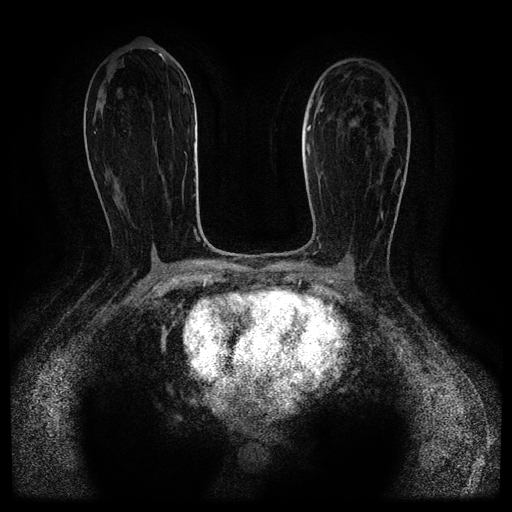
Breast MRI (dynamic contrast-enhanced, multi-phase), one axial slice; position 54 of 116 along the scan axis; dynamic contrast-enhanced series, time point 2 of 5 at this slice position (early post-contrast); 1.5 T; TE 2.6 ms, TR 5.3 ms; 2 mm slice thickness; 512 × 512 image matrix. Female patient, age 52 years.
Annotated regions visible in this slice (semi-automatically segmented with operator editing):
- breast lesion (labelled benign in the annotation): box from (x=351, y=122) to (x=355, y=126) px